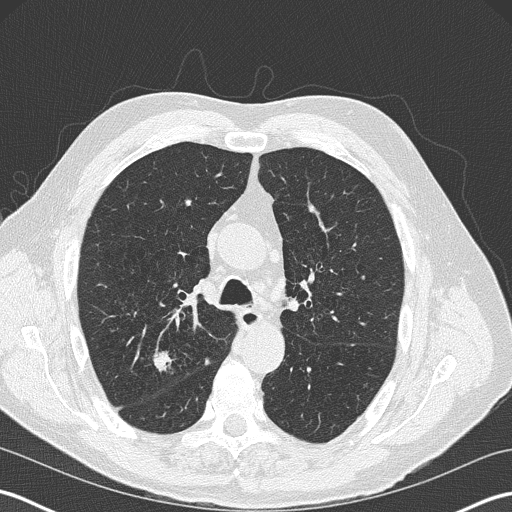
Low-dose screening chest CT, one axial slice. Position 128 of 199 along the scan axis. 120 kVp. One of 3 acquisitions stored at this slice position. Lung window (W 1500 / L -600 HU). 2 mm slice thickness. 512 × 512 image matrix.
Structures marked on this image (outlined manually by an expert reader):
- lesion 1 (tumor, upper lobe of right lung): bounding box (x1, y1, x2, y2) in pixels: (154, 352, 170, 370)